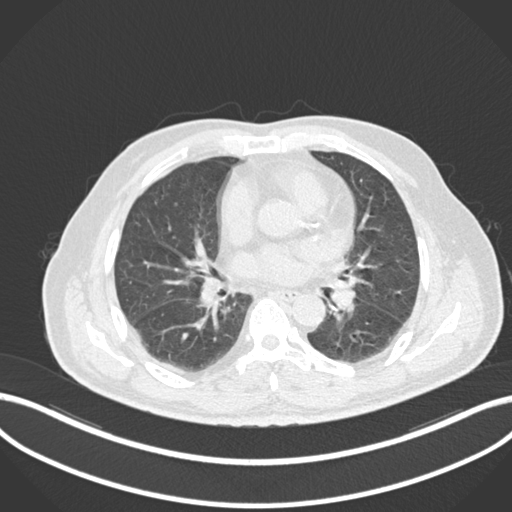
Chest CT, one axial slice; position 68 of 161 along the scan axis; reconstruction kernel B30f; 120 kVp; lung window (W 1500 / L -600 HU); 1 mm slice thickness; 512 × 512 image matrix. Male patient, age 71 years. From the clinical record (not read from this slice): clinical TNM (as recorded): T1b N0 M0.
Annotated regions visible in this slice (bounding box drawn by a radiologist):
- lung tumour (recorded histology: squamous cell carcinoma): bounding box [x1, y1, x2, y2] px = [328, 275, 357, 317]